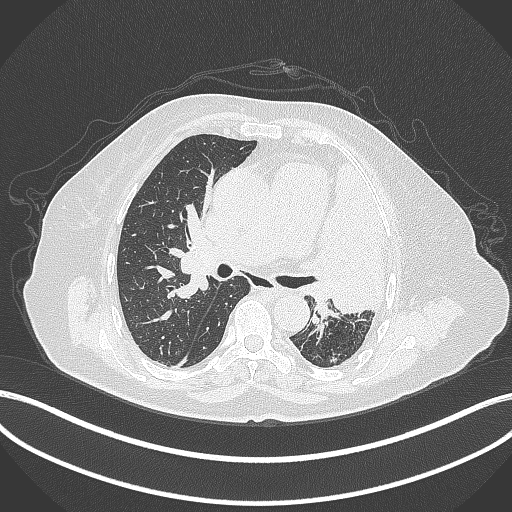
Chest CT, one axial slice; position 229 of 399 along the scan axis; 120 kVp; lung window (W 1500 / L -600 HU); 1 mm slice thickness; 512 × 512 image matrix, field of view 400 × 400 mm. Female patient, age 75 years. Case-level facts recorded for this patient, not image findings: clinical TNM (as recorded): T3 N3 M1.
Annotated regions visible in this slice (rectangle marked by the reading radiologist):
- lung tumour (recorded histology: adenocarcinoma): bounding box (x1, y1, x2, y2) in pixels: (306, 153, 402, 315)